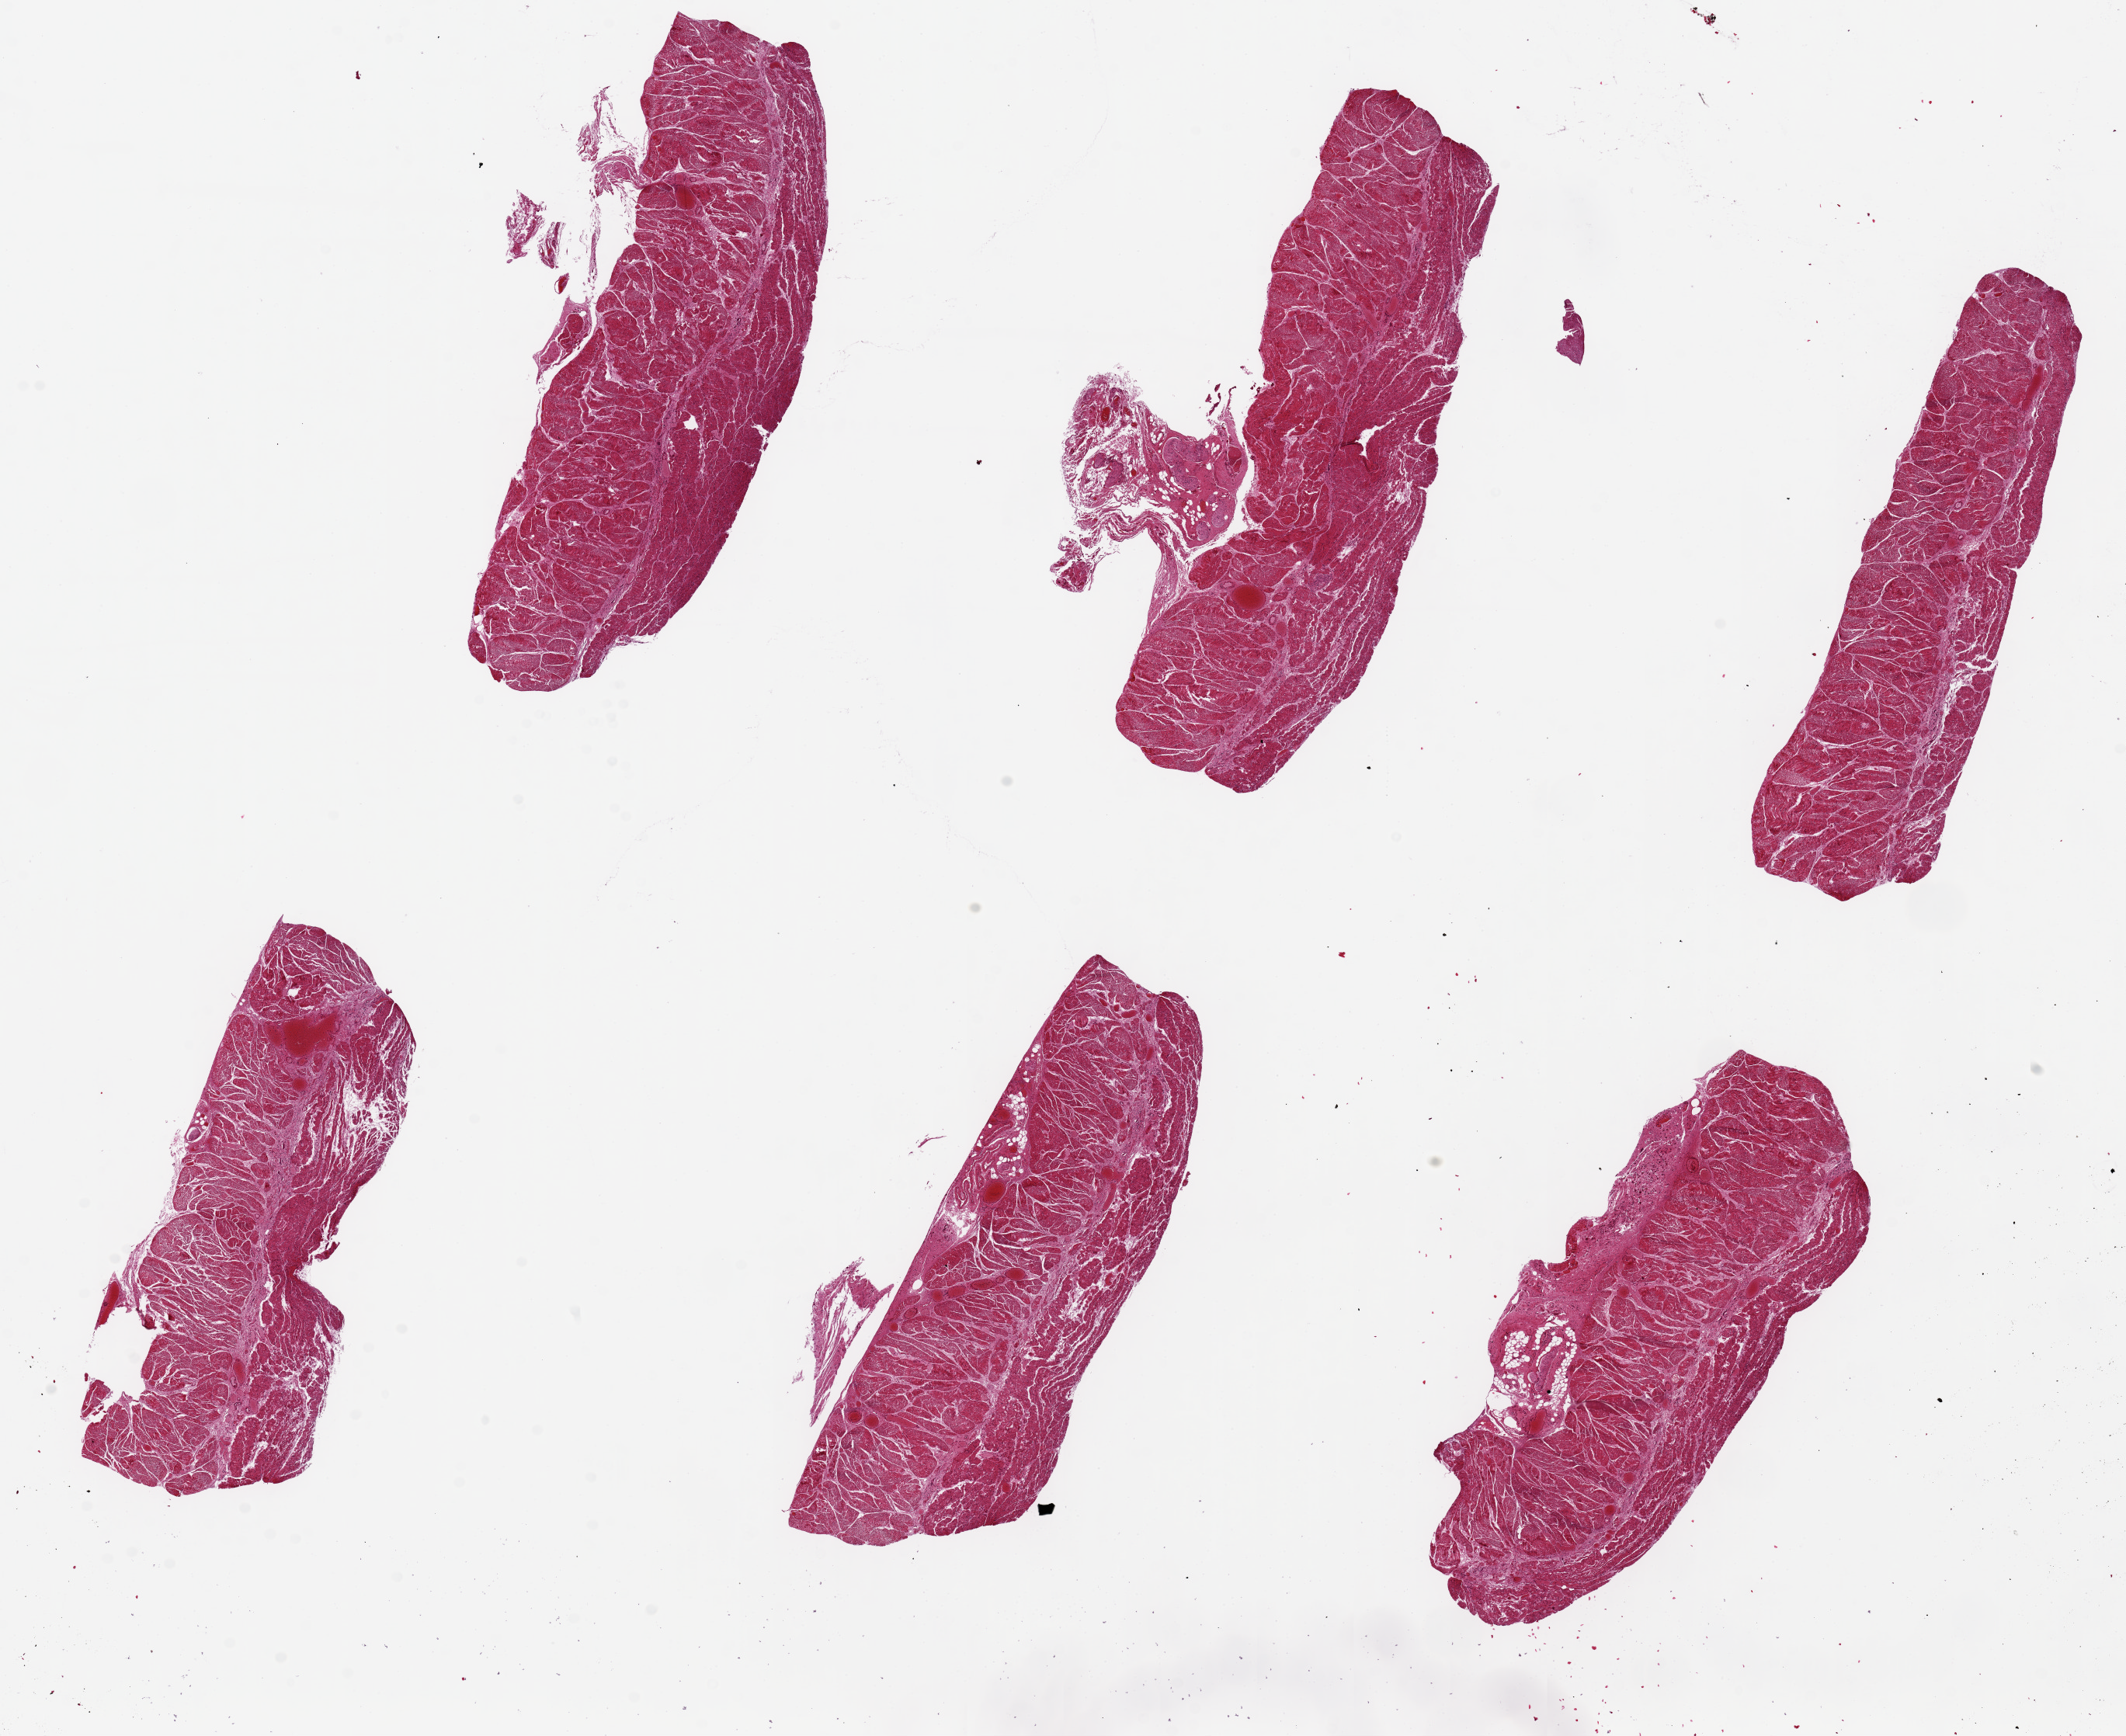
Whole-slide image, haematoxylin and eosin stain — a low-resolution overview of the entire scanned area, about 21.7 x 17.7 mm (slide scanned at 20x); PAXgene-fixed, paraffin-embedded tissue; section of esophageal muscle (target tissue); tissue donor sample.
Pathologist's review note for this sample: 6 pieces ~7x2mm, all muscuarlis.